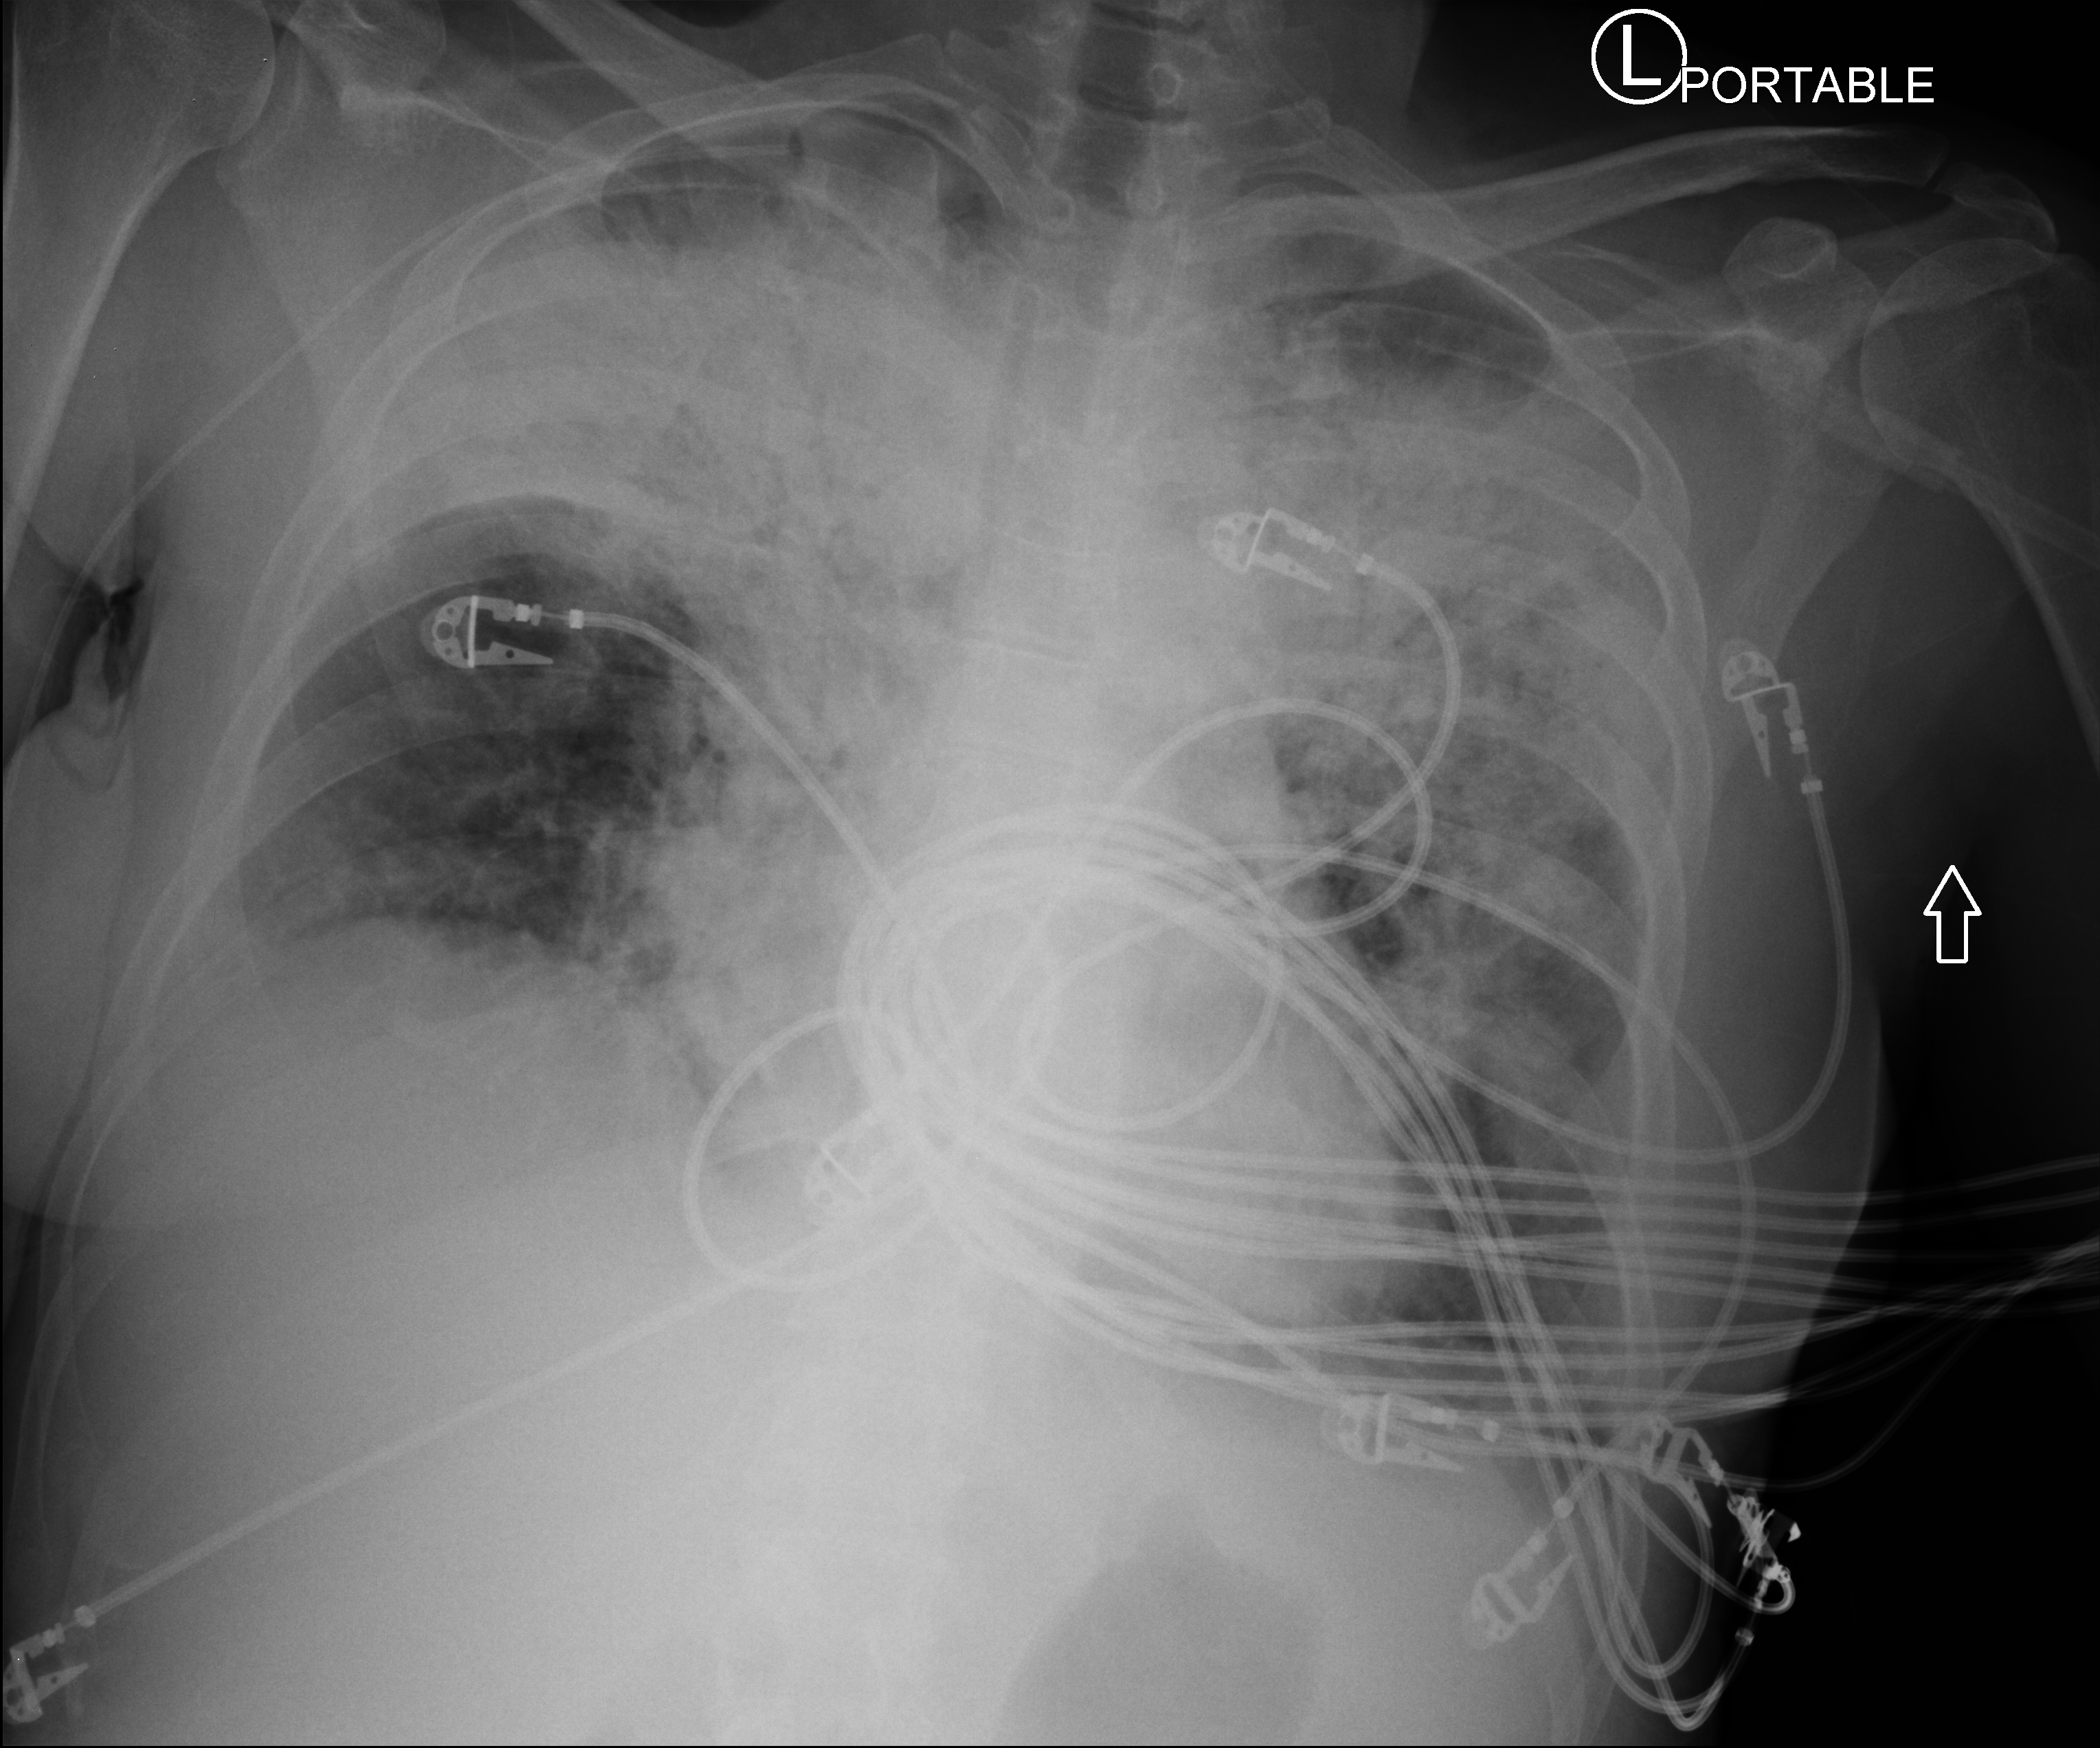
Bedside chest radiograph (computed radiography); anteroposterior (AP) projection. Female patient hospitalised with COVID-19, age 18–59 years.
Hospital-stay facts (about this admission, not read from this image; timing relative to this image not recorded):
- admitted to intensive care during this hospital stay: yes
- mechanically ventilated during this hospital stay: no
- hypertension (admission record): no